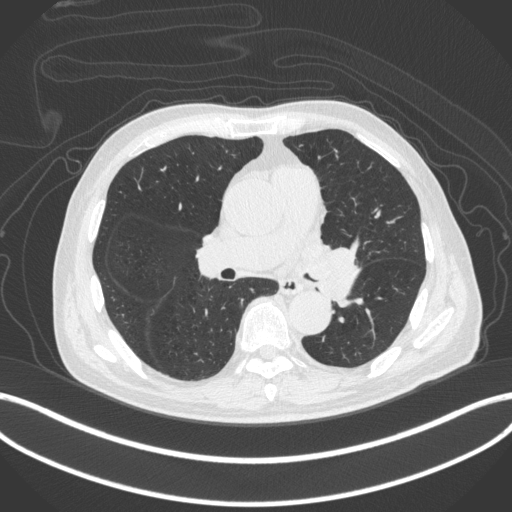
Chest CT, one axial slice. Position 236 of 420 along the scan axis. Reconstruction kernel B31f. 120 kVp. Lung window (W 1500 / L -600 HU). 1 mm slice thickness. 512 × 512 image matrix, field of view 400 × 400 mm. Patient: male, 77 years. From the clinical record (not read from this slice): clinical TNM (as recorded): T3 N1 M0.
Outlined on this slice (bounding box drawn by a radiologist):
- lung tumour (recorded histology: adenocarcinoma): bounding box <308,236,364,307> (left, top, right, bottom; pixels)